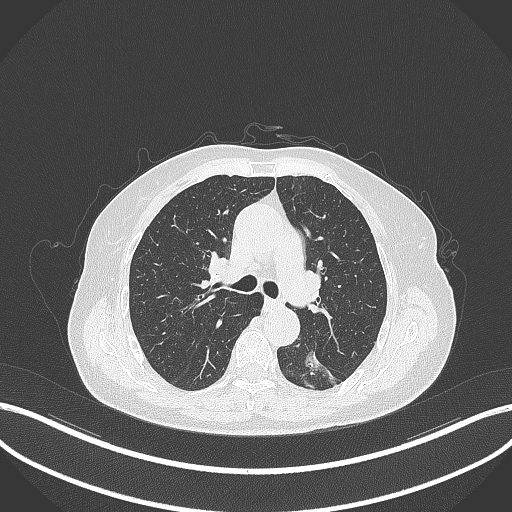
Chest CT, one axial slice. Reconstruction kernel B70f. 120 kVp. Lung window (W 1500 / L -600 HU). 1 mm slice thickness. 512 × 512 image matrix, field of view 400 × 400 mm. Patient: female, 70 years. Case-level facts recorded for this patient, not image findings: clinical TNM (as recorded): T1c N0 M0.
Structures marked on this image (bounding box drawn by a radiologist):
- lung tumour (recorded histology: adenocarcinoma): box from (x=298, y=341) to (x=328, y=377) px